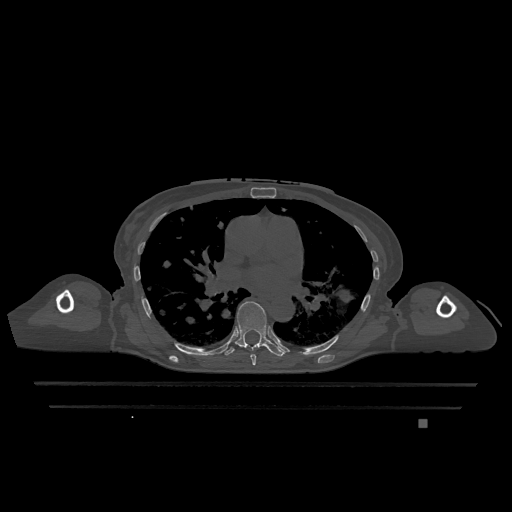
CT including the spine, one axial slice; position 755 of 1317 along the scan axis; bone window (W 1800 / L 400 HU); 0.5 mm slice thickness; 512 × 512 image matrix, field of view 500 × 500 mm. Female patient, age 74 years. From the clinical record (not read from this slice): primary cancer: lung; vertebrae with lytic lesions (as recorded): T1, T4, T5, T6, L4, L5.
Outlined on this slice (semi-automatically segmented with operator editing):
- T6 vertebra: box from (x=250, y=354) to (x=256, y=366) px
- T7 vertebra: (x=222, y=301)–(x=286, y=357)